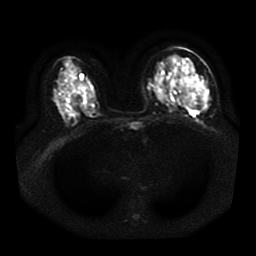
Breast MRI, one axial slice; slice 21 of 41 in the series (ordered by position); diffusion-weighted series; image 2 of 4 stored at this slice position (different b-values; order by instance number); 1.5 T; 5 mm slice thickness; 256 × 256 image matrix. Female patient.
Annotated regions visible in this slice (expert manual segmentation):
- tumour on diffusion-weighted imaging: bounding box (x1, y1, x2, y2) in pixels: (177, 75, 205, 108)